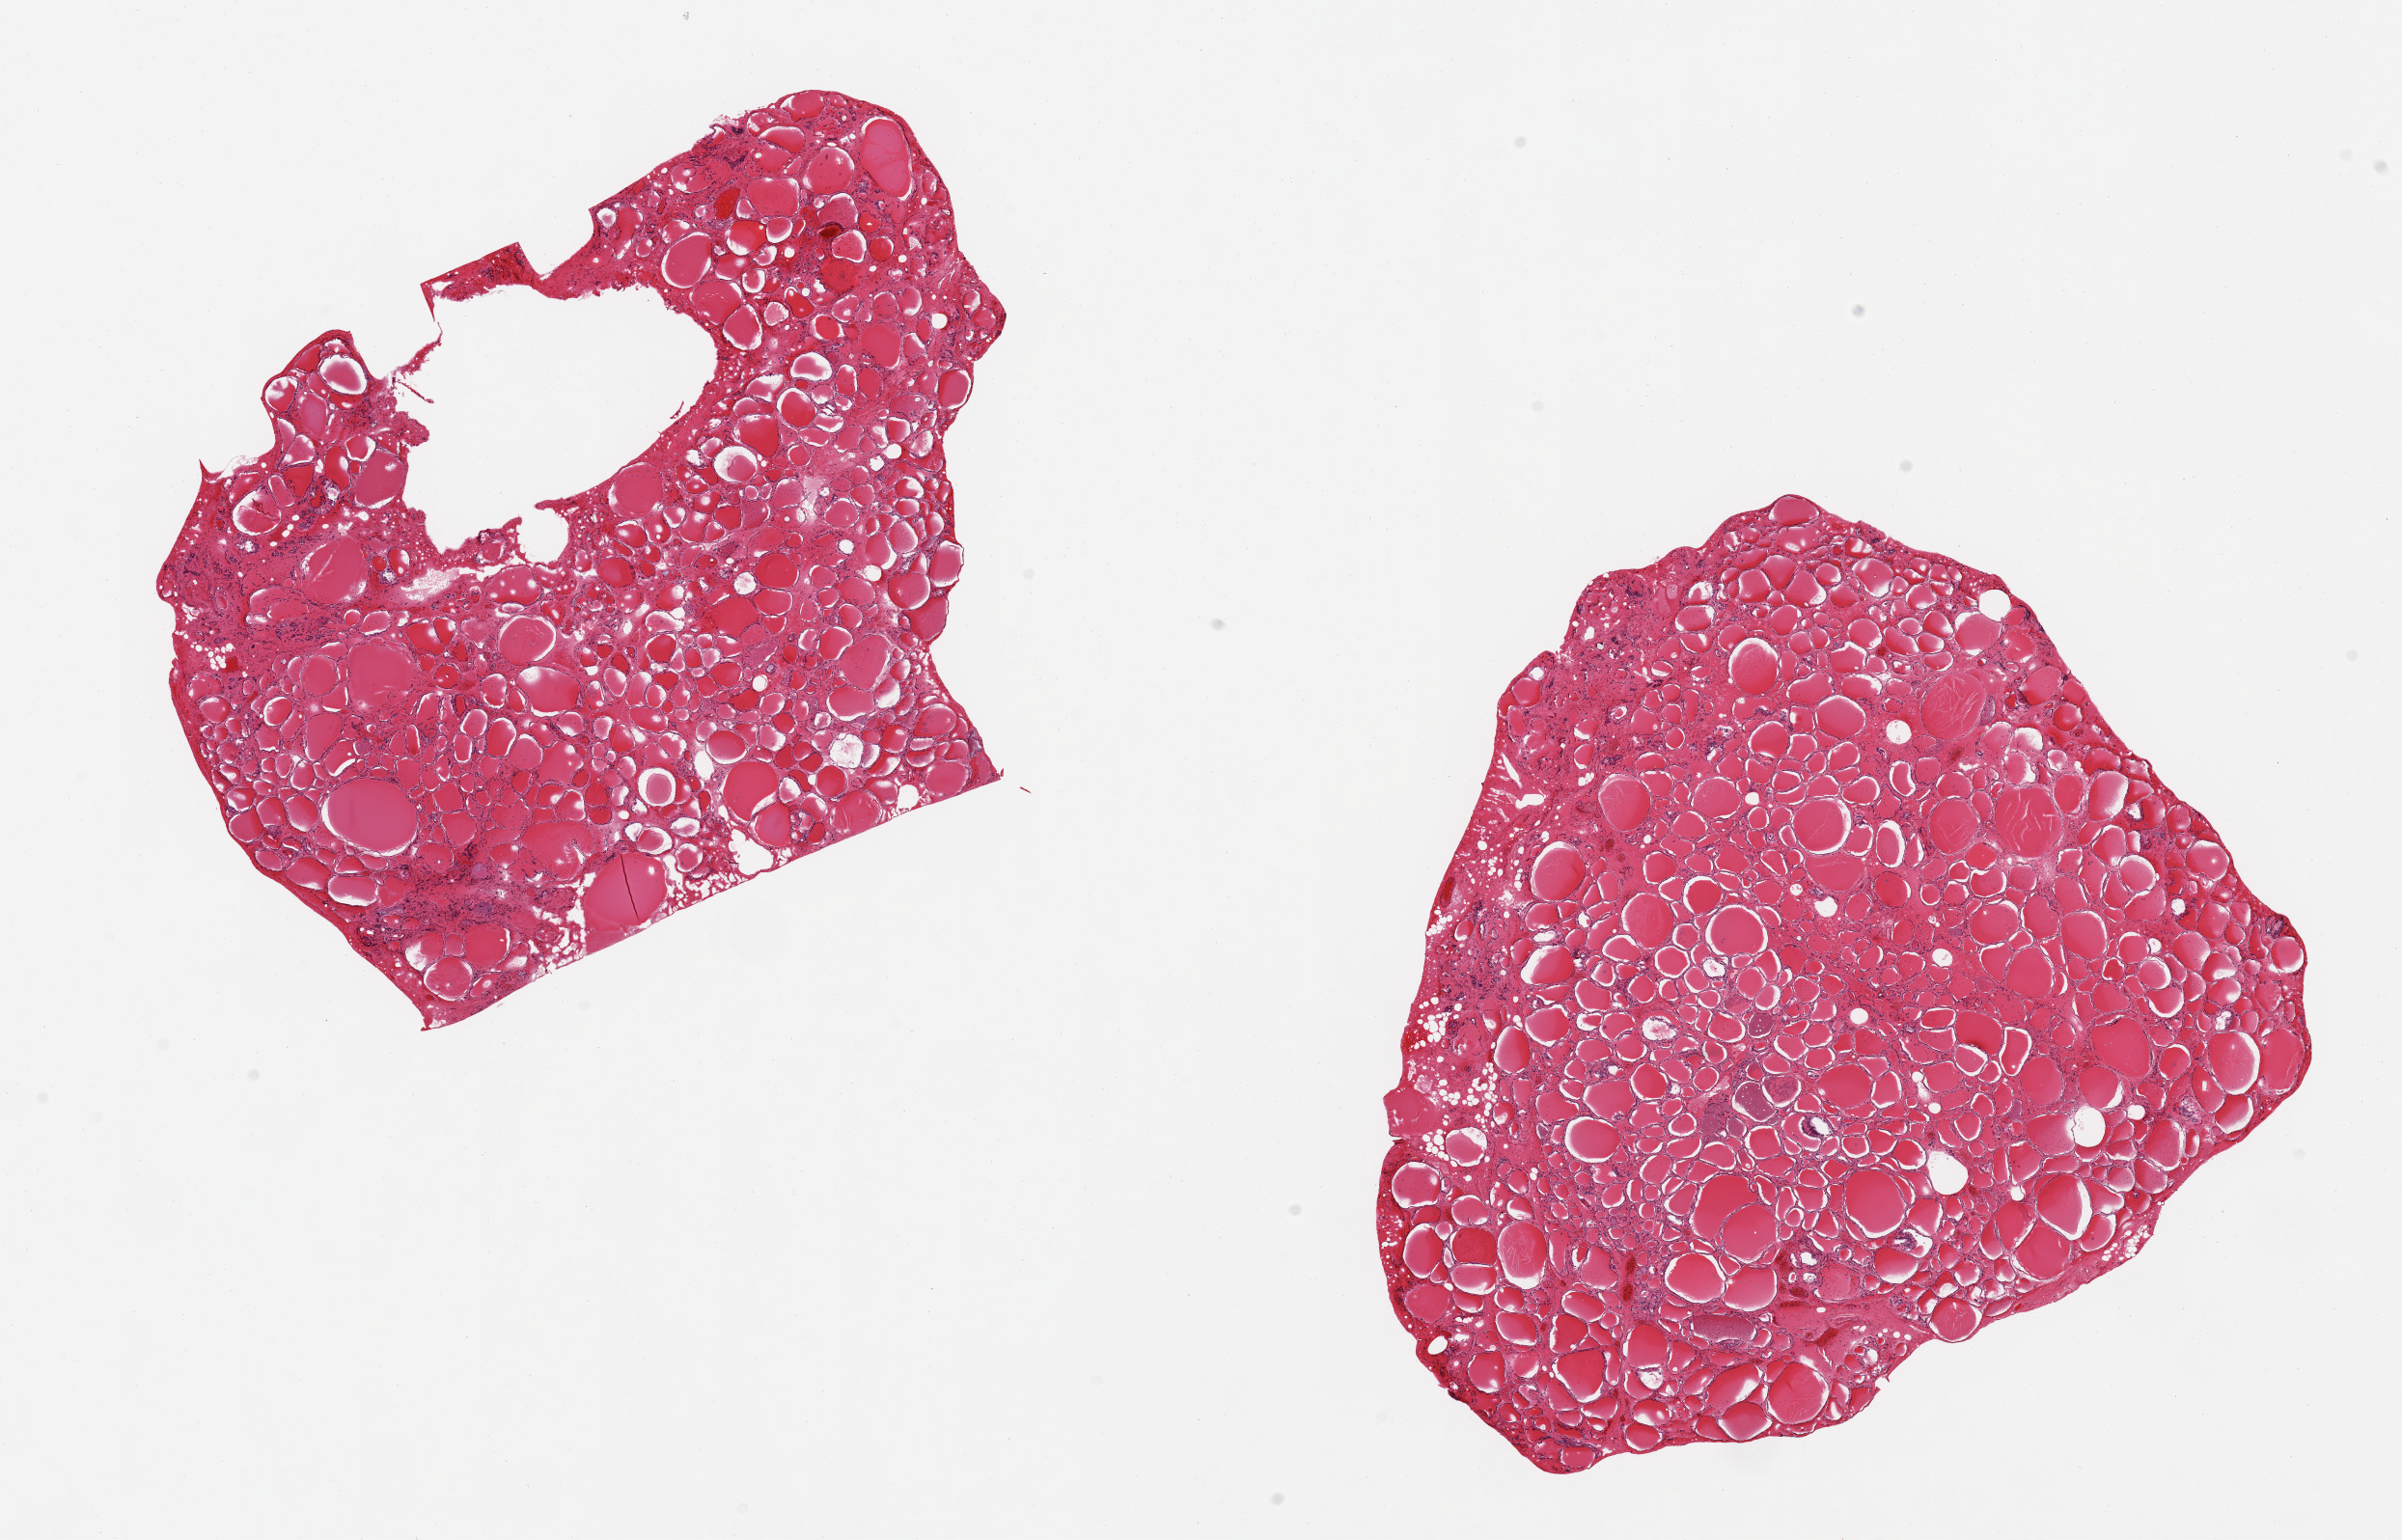
Whole-slide image, H&E stain, whole scanned area (about 19.7 x 12.6 mm) shown as a low-resolution overview; PAXgene-fixed paraffin-embedded (PFPE) section; section of thyroid (target tissue); donor tissue sample. Donor sex: male.
Reviewer comment on this tissue sample: 2 pieces, no abnormalities.